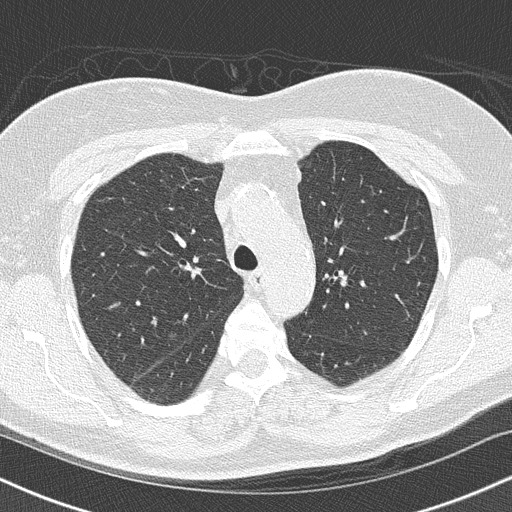
Low-dose screening chest CT, axial slice, baseline annual screen, lung window (W 1500 / L -600 HU), 2 mm slice thickness, lung (sharp) reconstruction kernel (B50f), slice 40 of 145 in the series, 512 × 512 image matrix. Female participant, aged 66 years at enrolment.
- Expert reader's lesion annotation, bounding box [x1, y1, x2, y2] px = [155, 326, 184, 346].
- Screening reader's record for this exam (one nodule recorded; not confirmed to be the boxed lesion): non-calcified nodule or mass ≥4 mm, right lower lobe, 10 × 8 mm, smooth margins, soft tissue attenuation.
- Official screen result: positive, change unspecified: nodule(s) >= 4 mm or enlarging nodule(s), mass(es), or other non-specific abnormalities suspicious for lung cancer.
- Participant outcome: lung cancer diagnosed 96 days after this screen — squamous cell carcinoma, keratinizing, NOS, right upper lobe, right middle lobe, poorly differentiated (G3), stage IA (AJCC 6th edition), 14 mm at pathology.